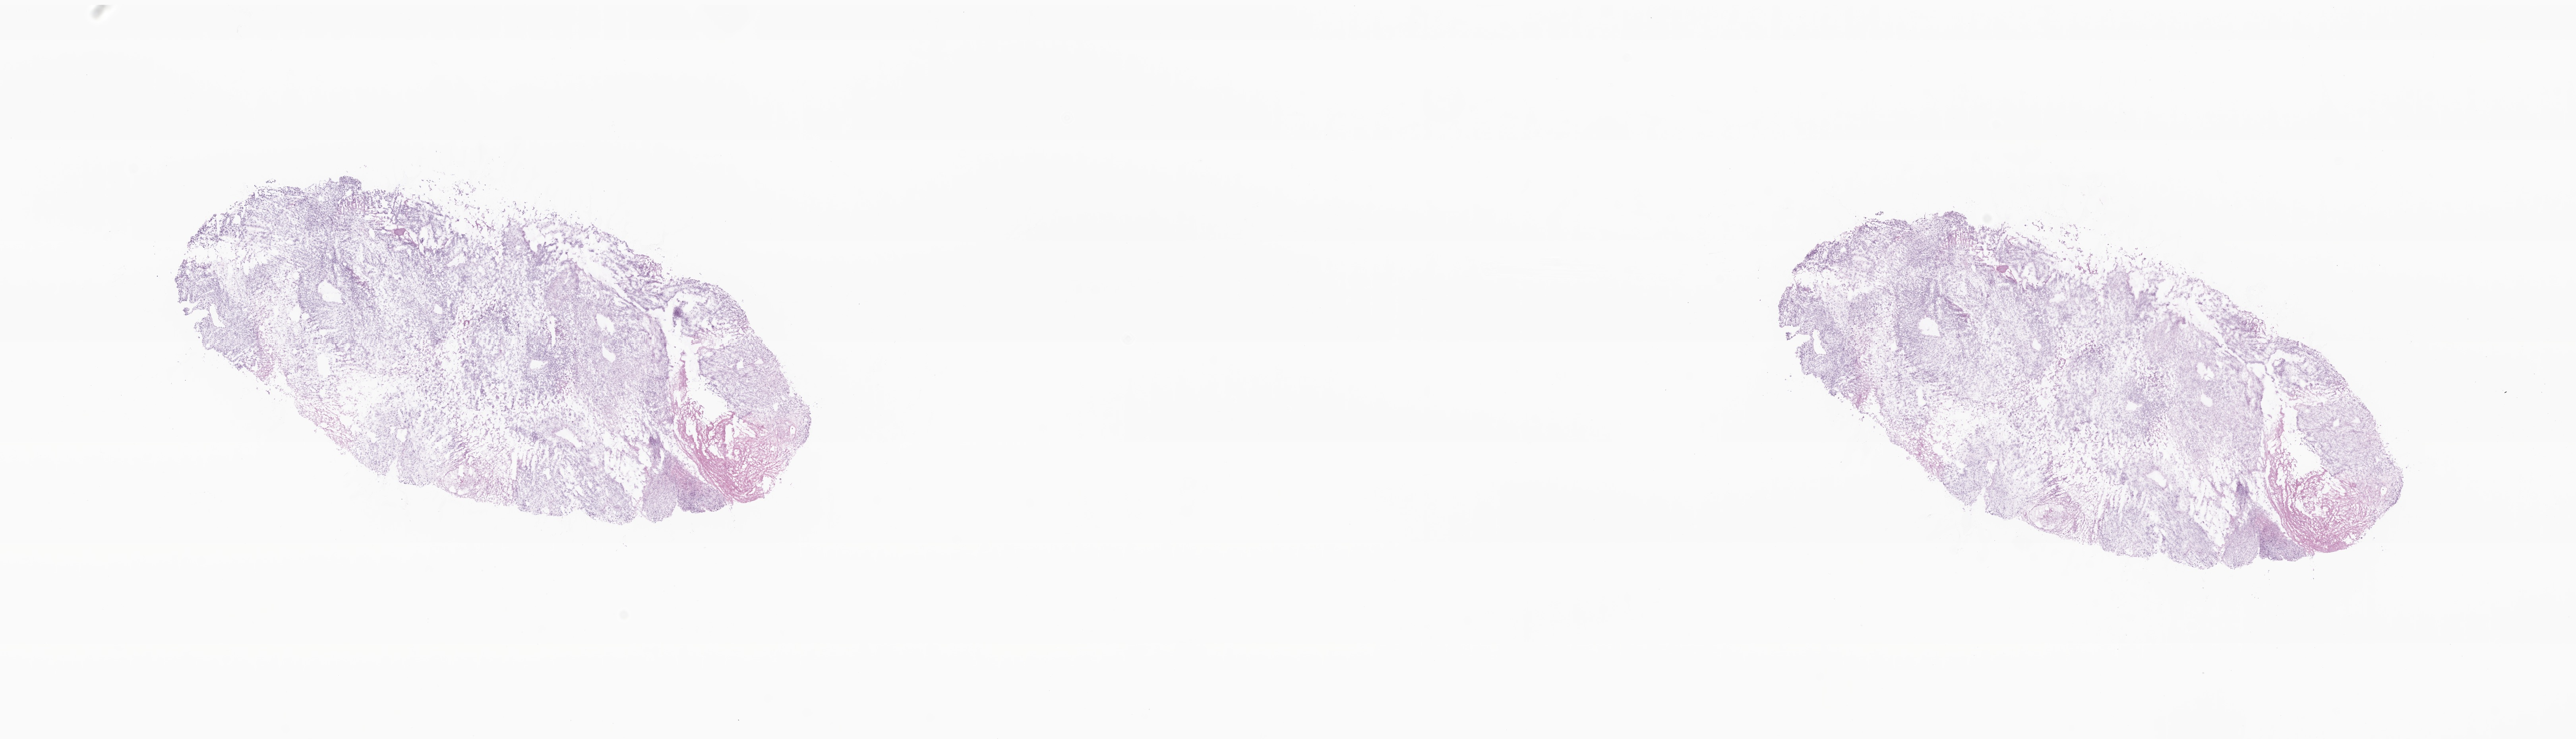
Digitized H&E-stained section — a low-resolution overview of the entire scanned area, about 27.3 x 7.8 mm. Cryosection. Primary tumor. Site: lung. Female, age 49 years at initial diagnosis. Composition of this section per pathologist review: tumor cells 85%, tumor nuclei 85%, stromal cells 10%, necrosis 5%, normal cells 0%. Infiltration values recorded for this section: lymphocyte infiltration 2%, monocyte infiltration 1%, neutrophil infiltration 2%.
Diagnosis: Leiomyosarcoma, NOS.